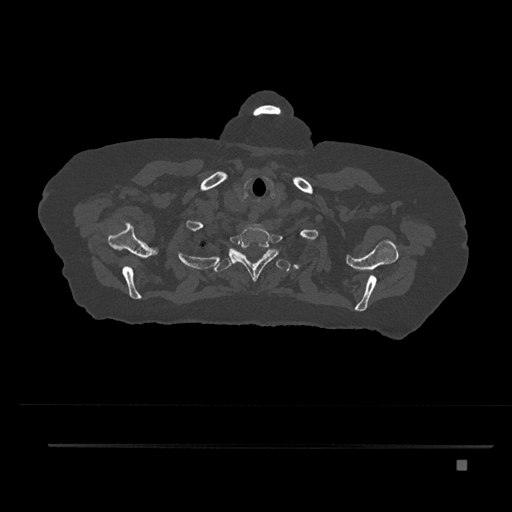
CT including the spine, one axial slice. 120 kVp. Bone window (W 1800 / L 400 HU). 0.5 mm slice thickness. 512 × 512 image matrix. Patient: female, 76 years. Case-level facts recorded for this patient, not image findings: primary cancer: lung; vertebrae with lytic lesions (as recorded): T11, L3.
Annotated regions visible in this slice (semi-automatically segmented with operator editing):
- T1 vertebra: box from (x=229, y=224) to (x=279, y=282) px
- T2 vertebra: (x=207, y=248)–(x=291, y=272)